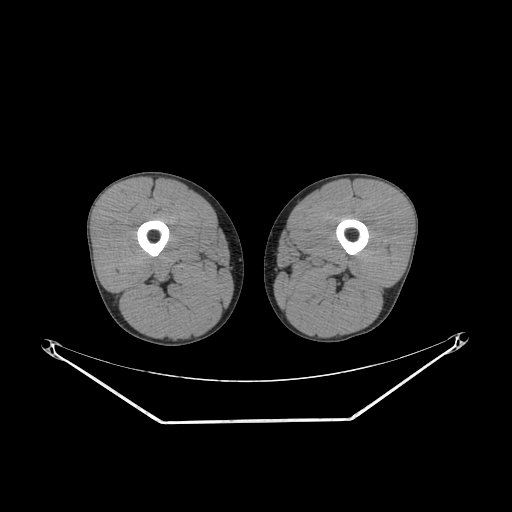
CT of an extremity soft-tissue mass (from a PET/CT study), one axial slice. Position 214 of 267 along the scan axis. Reconstruction kernel SOFT. 140 kVp. Soft-tissue window (W 400 / L 40 HU). 512 × 512 image matrix, field of view 500 × 500 mm. Male patient. Case-level facts recorded for this patient, not image findings: histological type: extraskeletal osteosarcoma; grade: high; site of the primary tumour: left adductur.
Outlined on this slice (expert contour drawn on MRI and transferred to this co-registered scan by the dataset authors):
- gross tumour volume (mass): bounding box (x1, y1, x2, y2) in pixels: (329, 256, 348, 268)